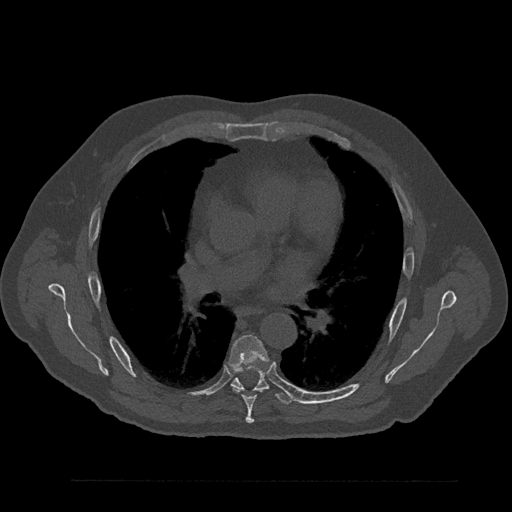
CT including the spine, one axial slice. Position 534 of 797 along the scan axis. Reconstruction kernel Br40s/3. Bone window (W 1800 / L 400 HU). 512 × 512 image matrix, field of view 430 × 430 mm. Male patient, age 61 years. Case-level facts recorded for this patient, not image findings: primary cancer: prostate.
Structures marked on this image (semi-automatic segmentation, software-assisted and operator-edited):
- T6 vertebra: box from (x=229, y=335) to (x=268, y=424) px
- T7 vertebra: (x=231, y=369)–(x=293, y=405)